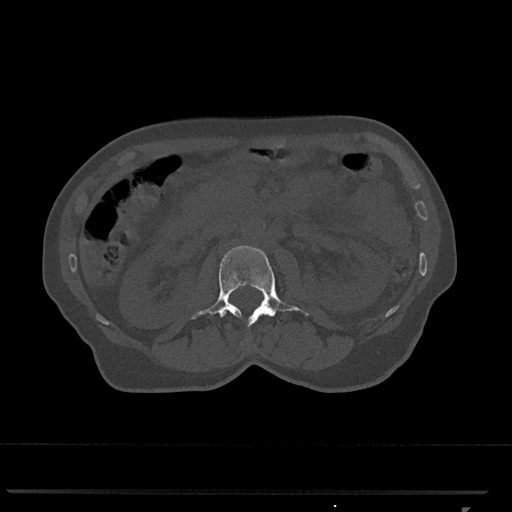
CT including the spine, one axial slice; 120 kVp; bone window (W 1800 / L 400 HU); 0.5 mm slice thickness; 512 × 512 image matrix, field of view 380 × 380 mm. Patient: female, 62 years. Case-level facts recorded for this patient, not image findings: primary cancer: renal.
Outlined on this slice (semi-automatically segmented with operator editing):
- L2 vertebra: box from (x=191, y=245) to (x=308, y=327) px